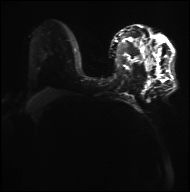
Breast MRI, one axial slice; position 20 of 36 along the scan axis; diffusion-weighted series; image 2 of 4 stored at this slice position (different b-values; order by instance number); 3 T; 190 × 192 image matrix, field of view 317 × 320 mm. Female patient.
Structures marked on this image (manually delineated by an expert):
- tumour on diffusion-weighted imaging: bounding box <0,44,63,79> (left, top, right, bottom; pixels)